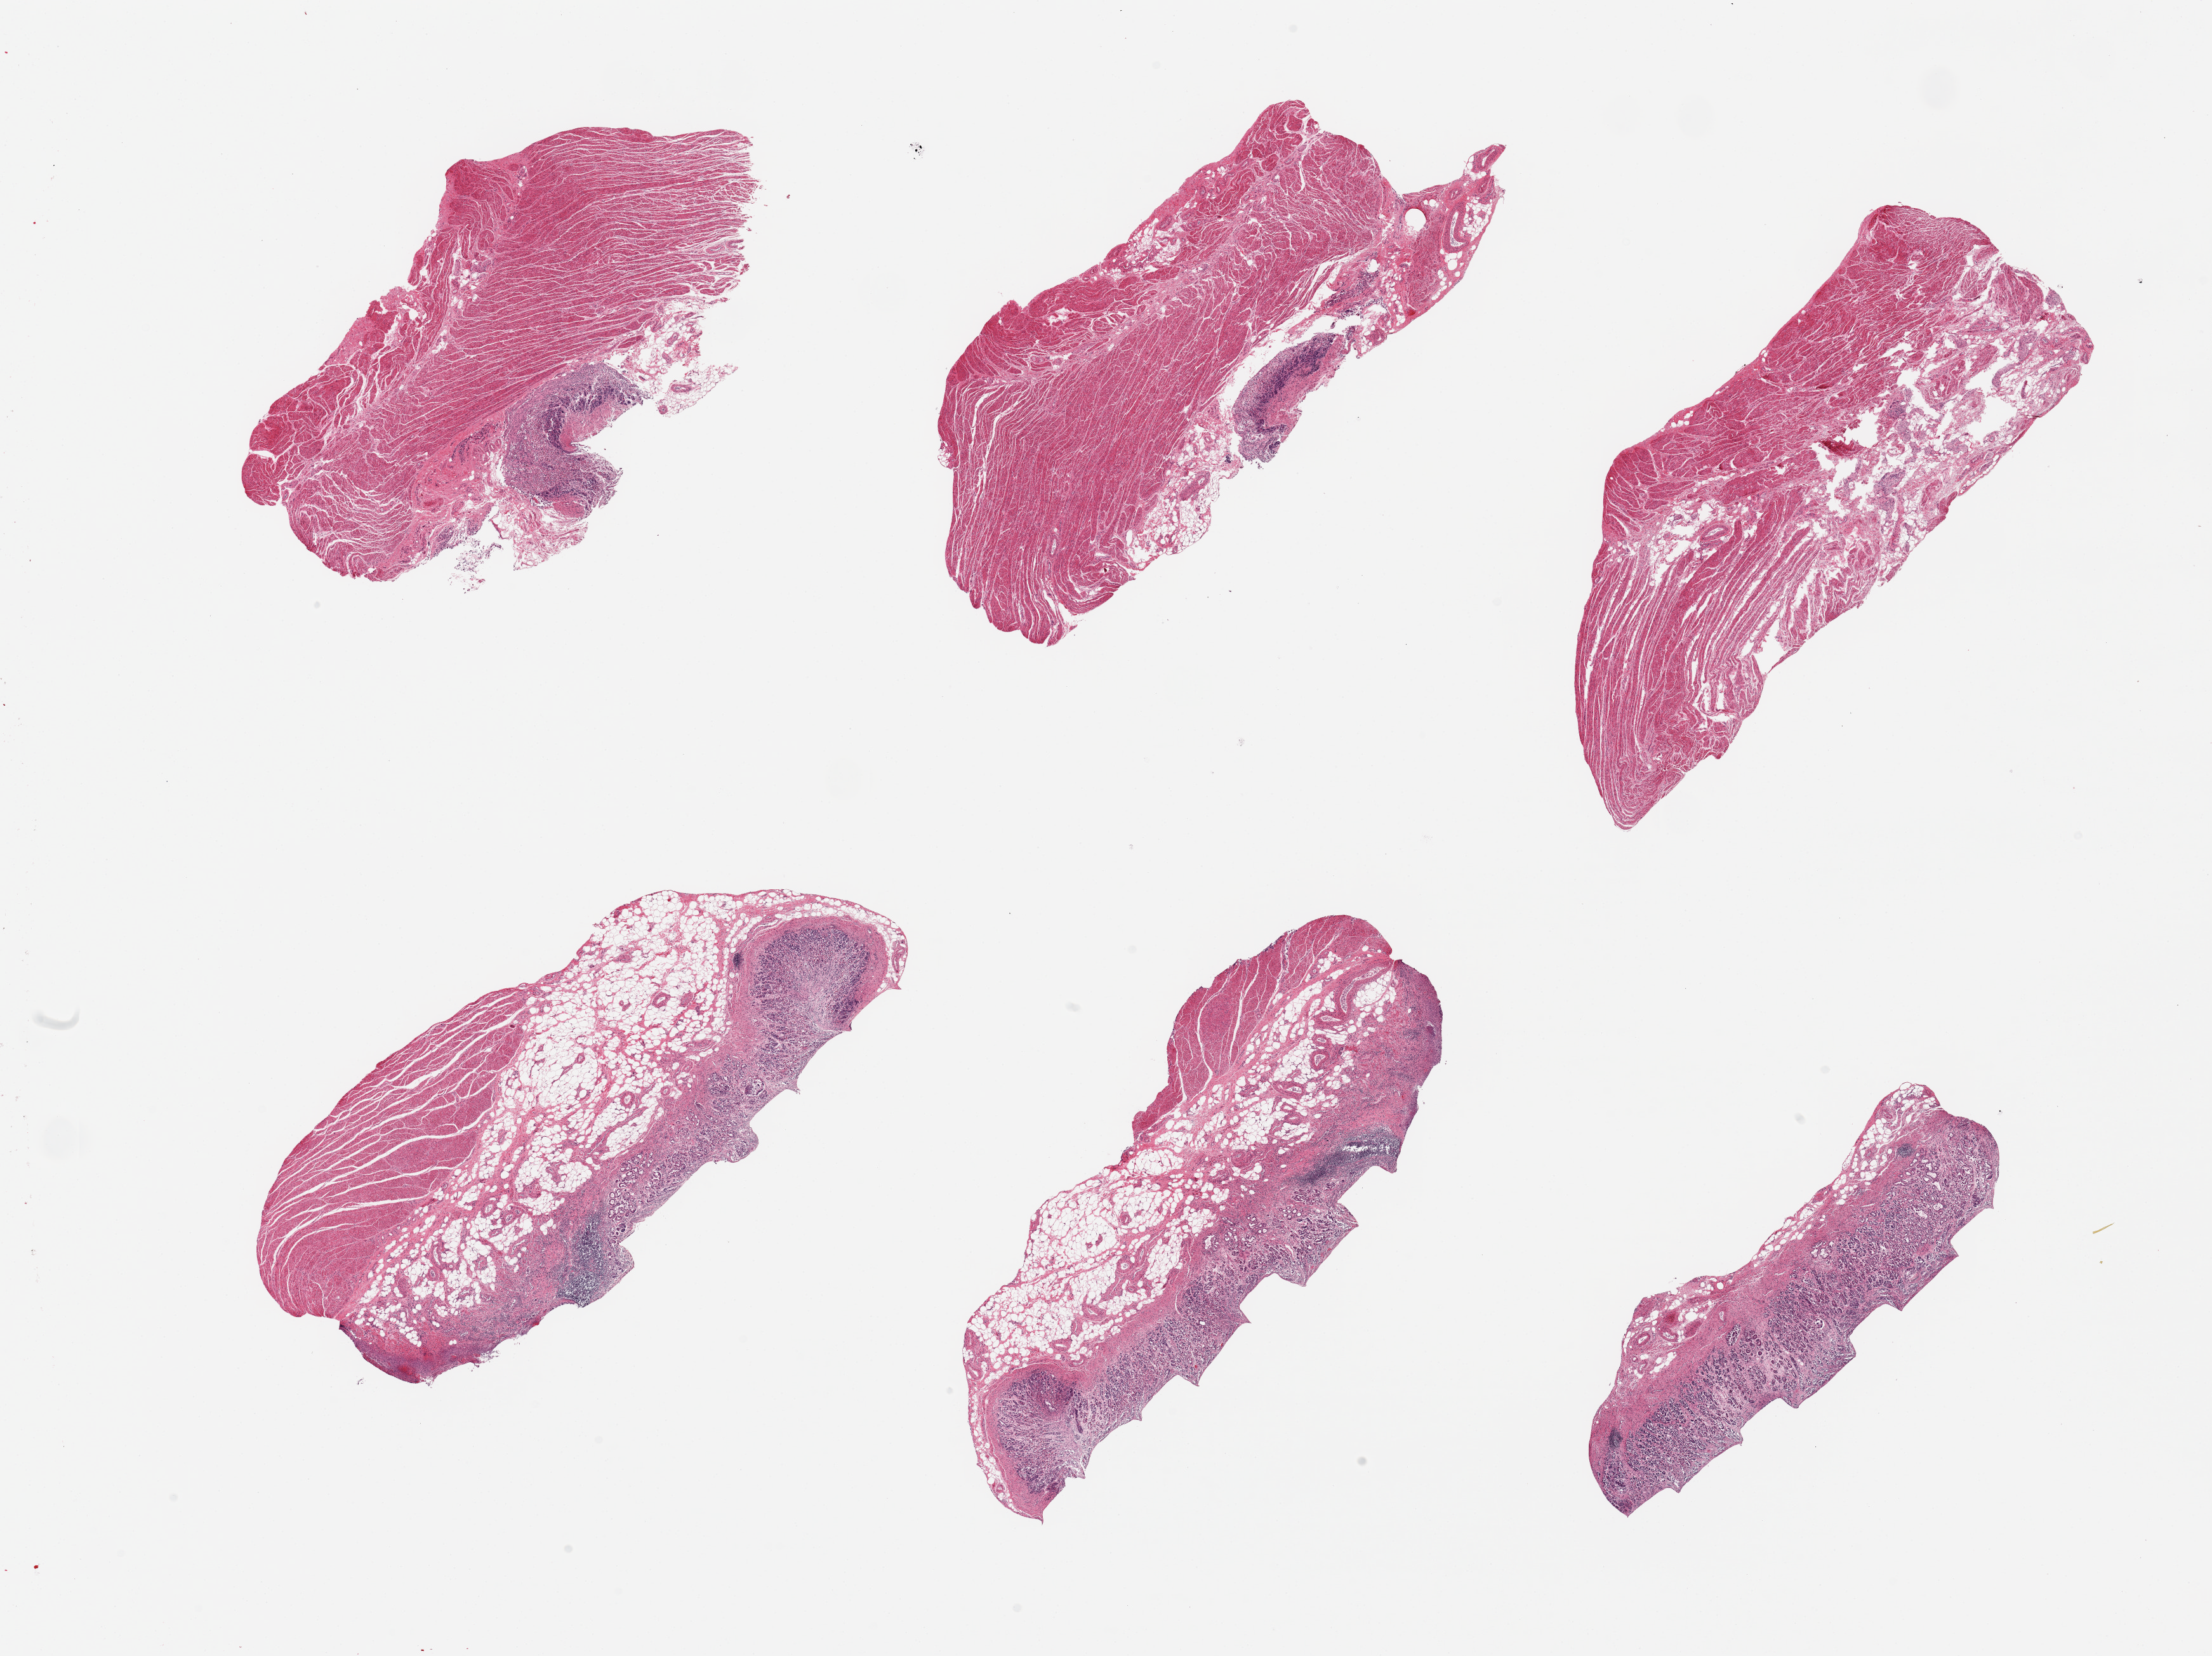
Whole-slide image, H&E stain, brightfield, shown as a low-resolution overview of the whole scanned area (about 27.6 x 20.6 mm, acquisition: 20x scan). PAXgene-fixed paraffin-embedded (PFPE) section. Sampled site (target tissue): gastroesophageal junction. Donor tissue sample. Donor: male.
Review note (as recorded): 6 pieces, mucosa present, 20-30% thickness, autolyzed, gastric type, incorrect target.